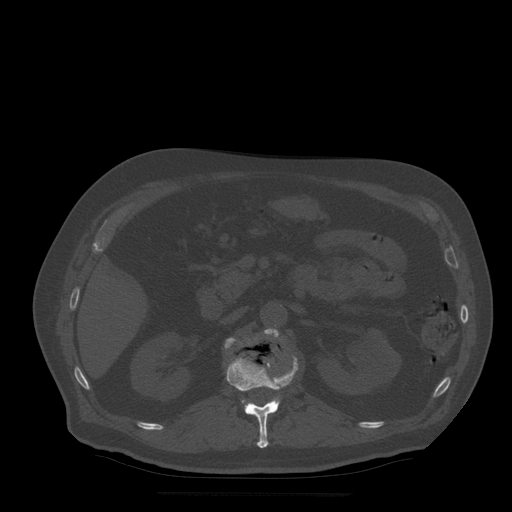
CT including the spine, one axial slice. Slice 189 of 522 in the series (ordered by position). Bone window (W 1800 / L 400 HU). 512 × 512 image matrix. Patient age 72 years. Case-level facts recorded for this patient, not image findings: primary cancer: prostate.
Annotated regions visible in this slice (semi-automatically segmented with operator editing):
- L1 vertebra: bounding box [x1, y1, x2, y2] px = [225, 338, 299, 449]
- L2 vertebra: [265, 329, 280, 414]